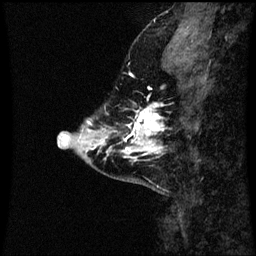
Breast MRI (dynamic contrast-enhanced), one sagittal slice. Slice 14 of 60 in the series (ordered by position). Dynamic contrast-enhanced series, image 2 of 3 at this slice position (ordered by acquisition). 1.5 T. TE 4.2 ms, TR 8.9 ms. 256 × 256 image matrix. Female patient, age 43 years. Case-level facts recorded for this patient, not image findings: setting: breast cancer imaged before/during neoadjuvant chemotherapy; receptor status: HR-positive, HER2-negative.
Outlined on this slice (semi-automatic segmentation, software-assisted and operator-edited):
- analysis volume of interest (the breast-tissue region the enhancement analysis was run in; not a lesion): bounding box [x1, y1, x2, y2] px = [110, 102, 164, 163]
- tumour enhancement mask (voxels above the 70 % enhancement threshold inside the analysis volume of interest): [121, 104, 164, 161]